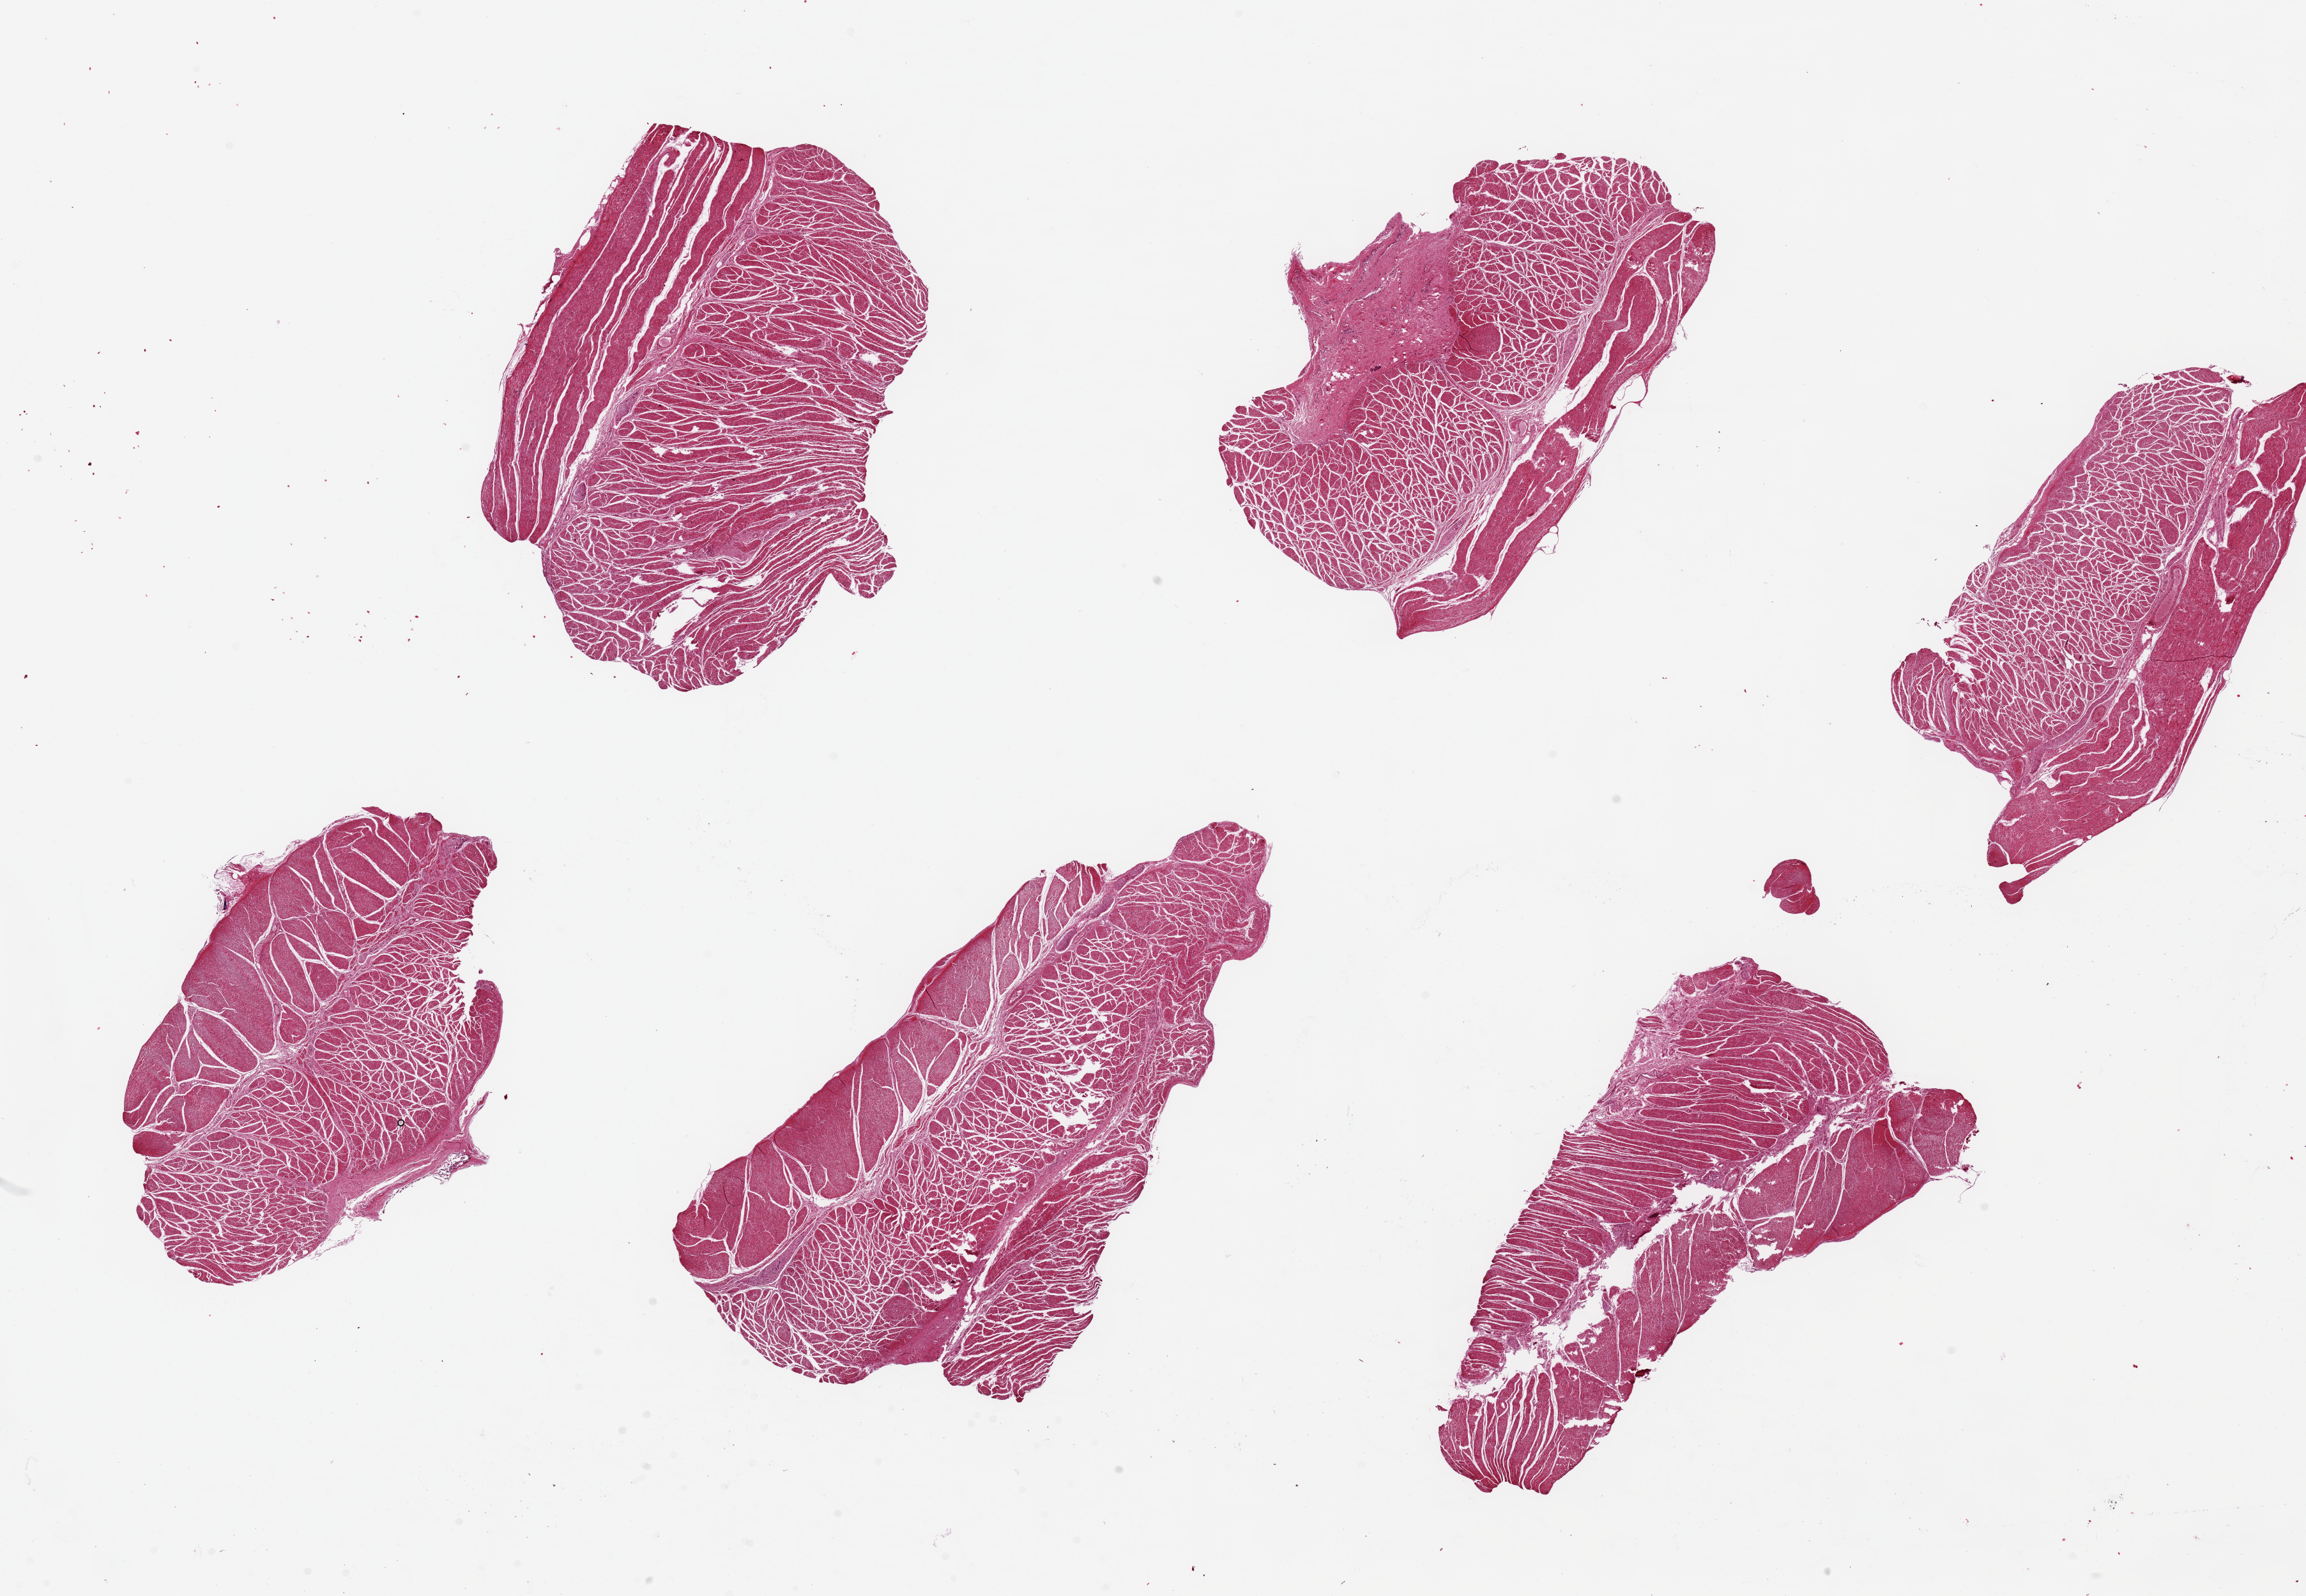
Whole-slide image, hematoxylin and eosin (H&E) stain — low-resolution overview of the scanned area, about 28.5 x 19.8 mm (slide scanned at 20x). PAXgene-fixed paraffin-embedded (PFPE) section. Section of esophageal muscle (target tissue). Tissue donor sample. Male donor.
- review note (as recorded): 6 pieces, up to 9x5mm; All muscle (target)